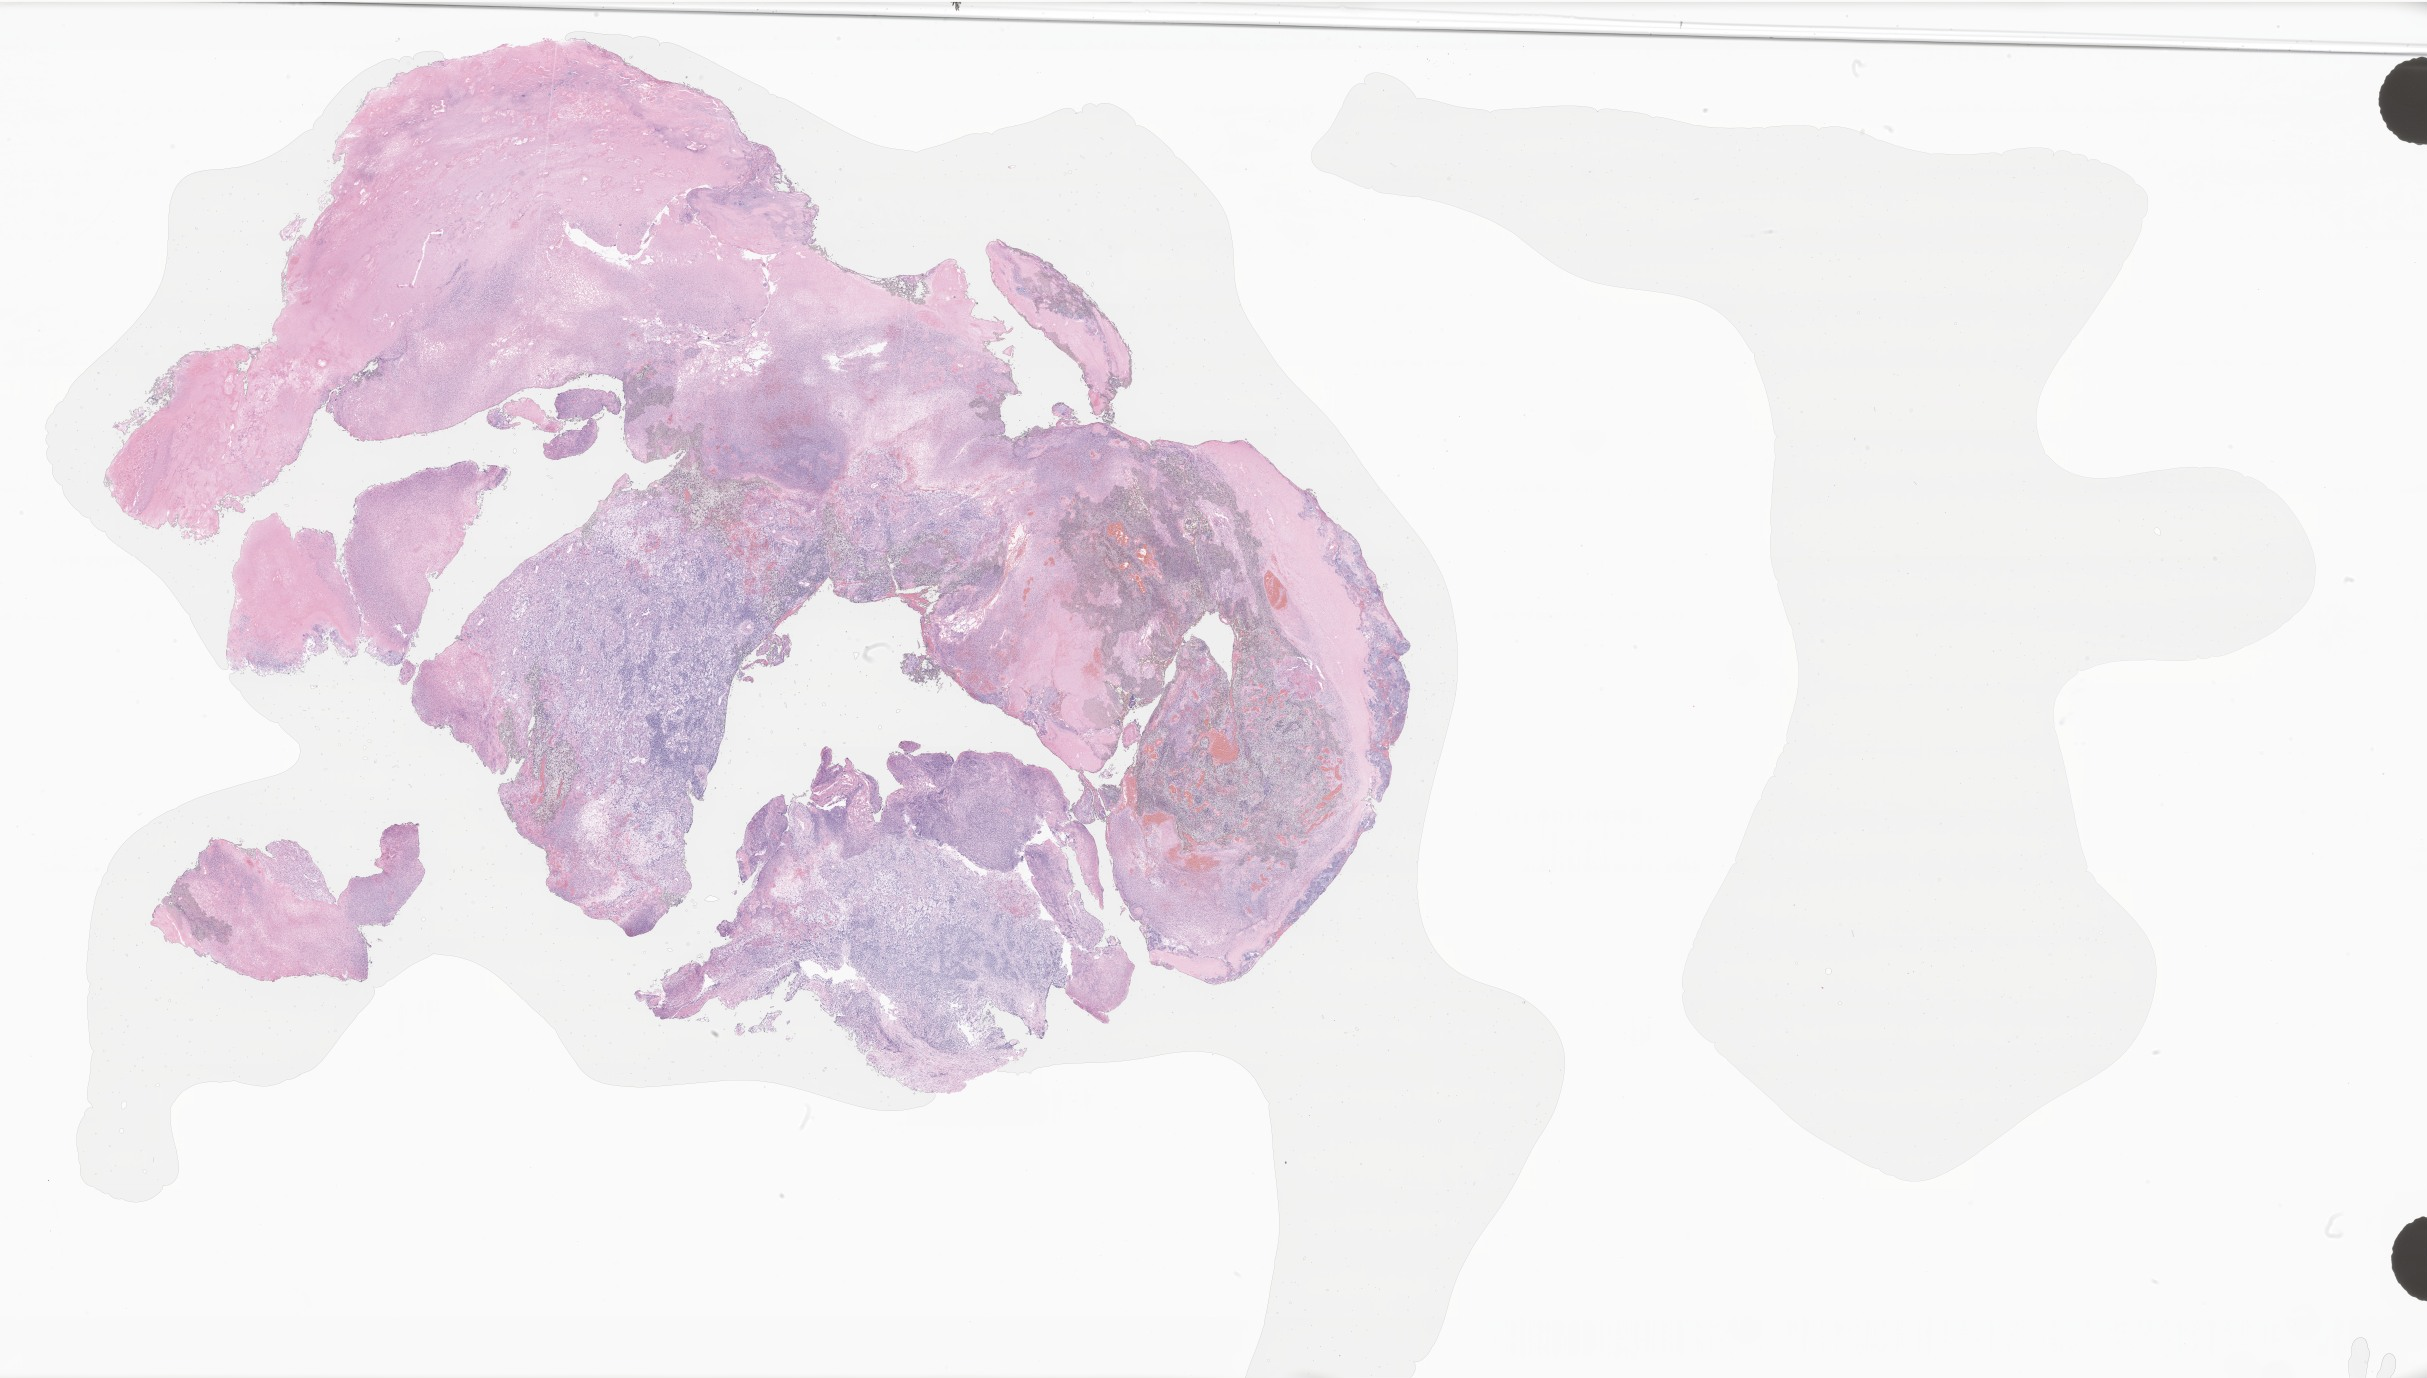
Digitized hematoxylin and eosin (H&E)-stained section of tumor tissue from the nasal cavity — shown as a low-resolution overview of the whole scanned area (about 40.9 x 23.2 mm); formalin-fixed paraffin-embedded section. Patient male; age 59 months.
• diagnosis (ICD-O-3 morphology term): Embryonal rhabdomyosarcoma, NOS